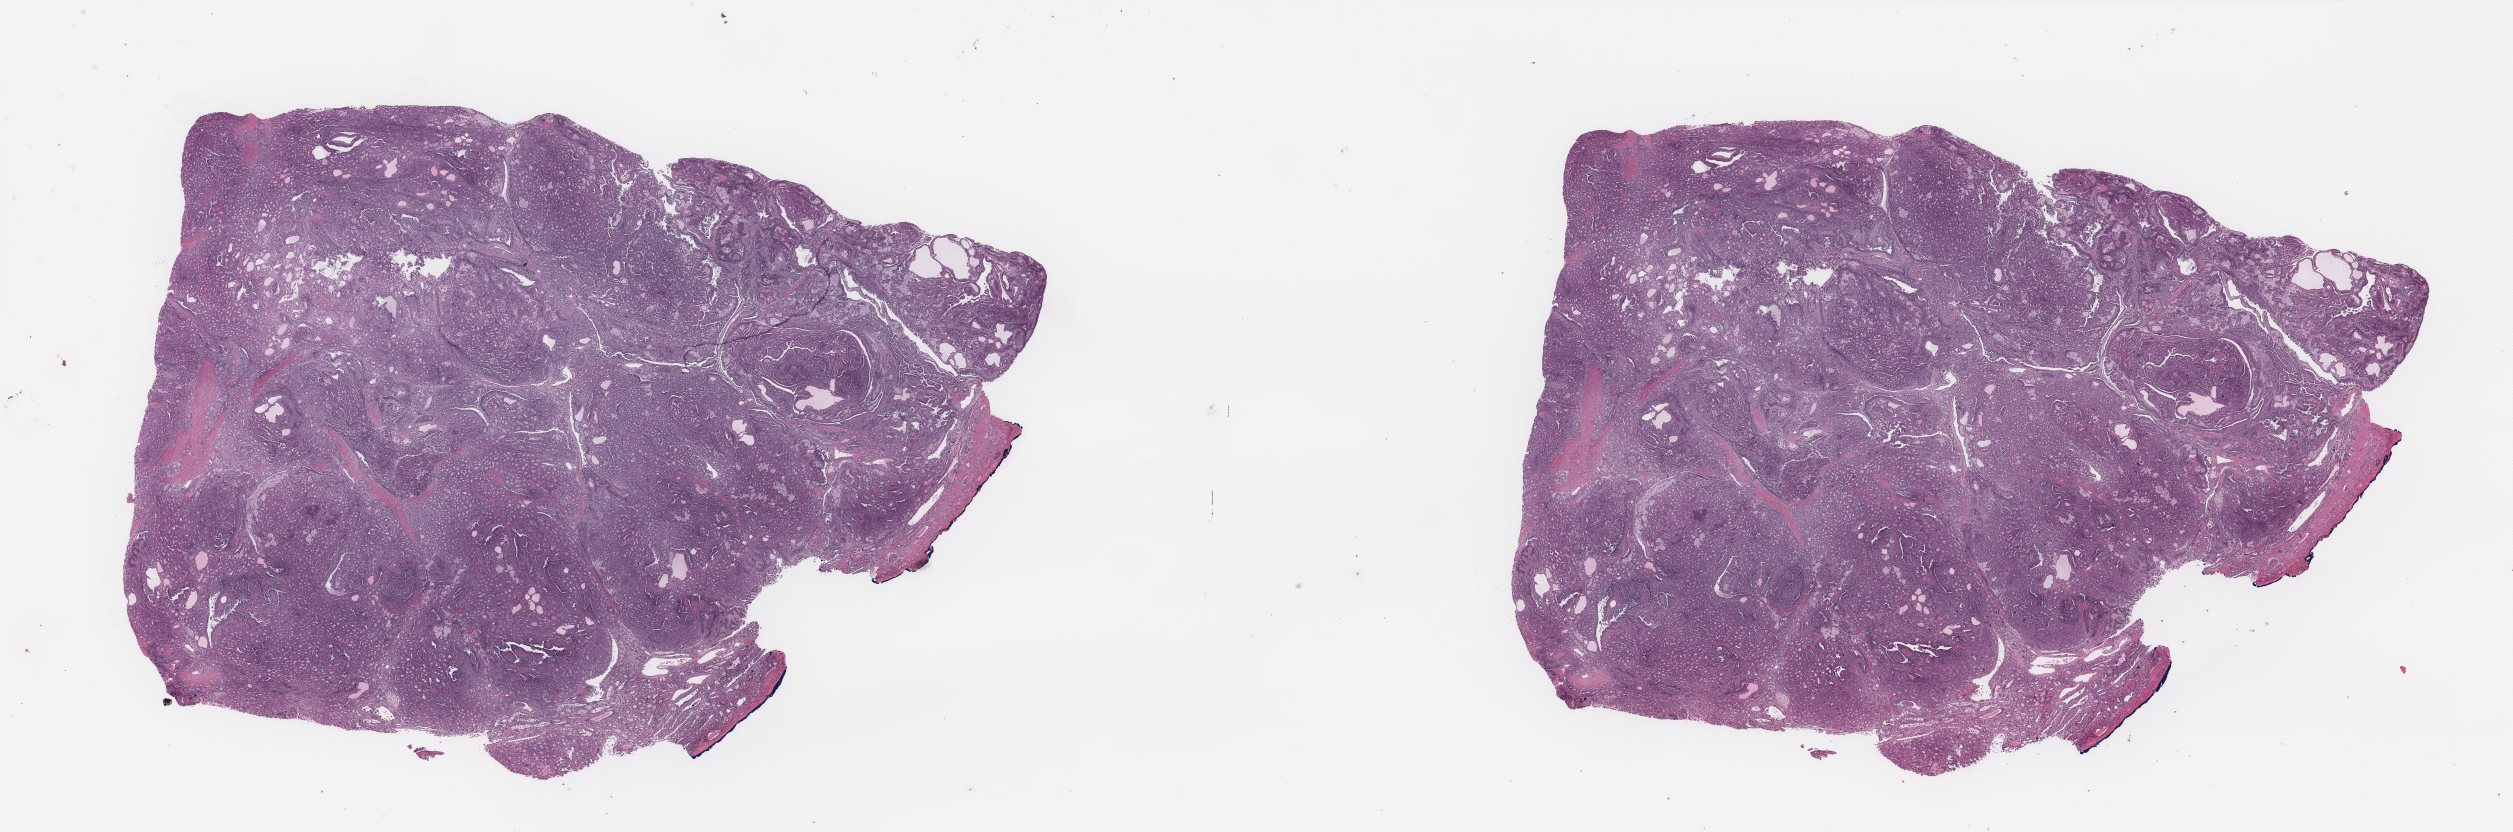
Digitized H&E tissue section (whole slide), low-resolution overview of the scanned area, about 39.8 x 13.2 mm (slide scanned at 40x); formalin-fixed paraffin-embedded (FFPE) diagnostic section; sample: primary tumour, kidney. Patient: male, age at initial diagnosis 40 years.
• AJCC pathologic stage: I (7th edition)
• laterality: right
• pathologic diagnosis: Papillary adenocarcinoma, NOS